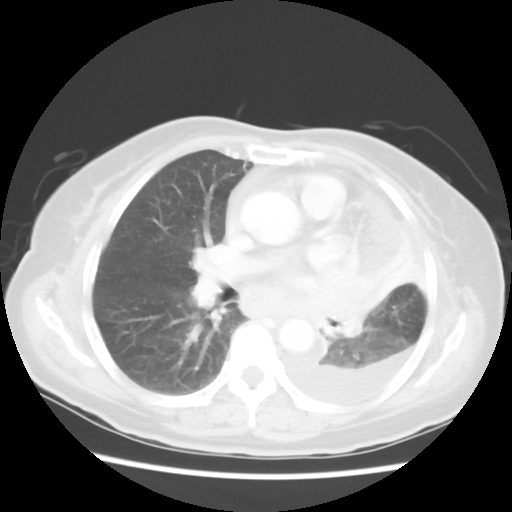
Chest CT, one axial slice; reconstruction kernel STANDARD; lung window (W 1500 / L -600 HU); 5 mm slice thickness; 512 × 512 image matrix, field of view 336 × 336 mm. Female patient, age 72 years. Case-level facts recorded for this patient, not image findings: clinical TNM (as recorded): T4 N3 M1b.
Structures marked on this image (bounding box drawn by a radiologist):
- lung tumour (recorded histology: large cell carcinoma): bounding box [x1, y1, x2, y2] px = [304, 260, 378, 343]